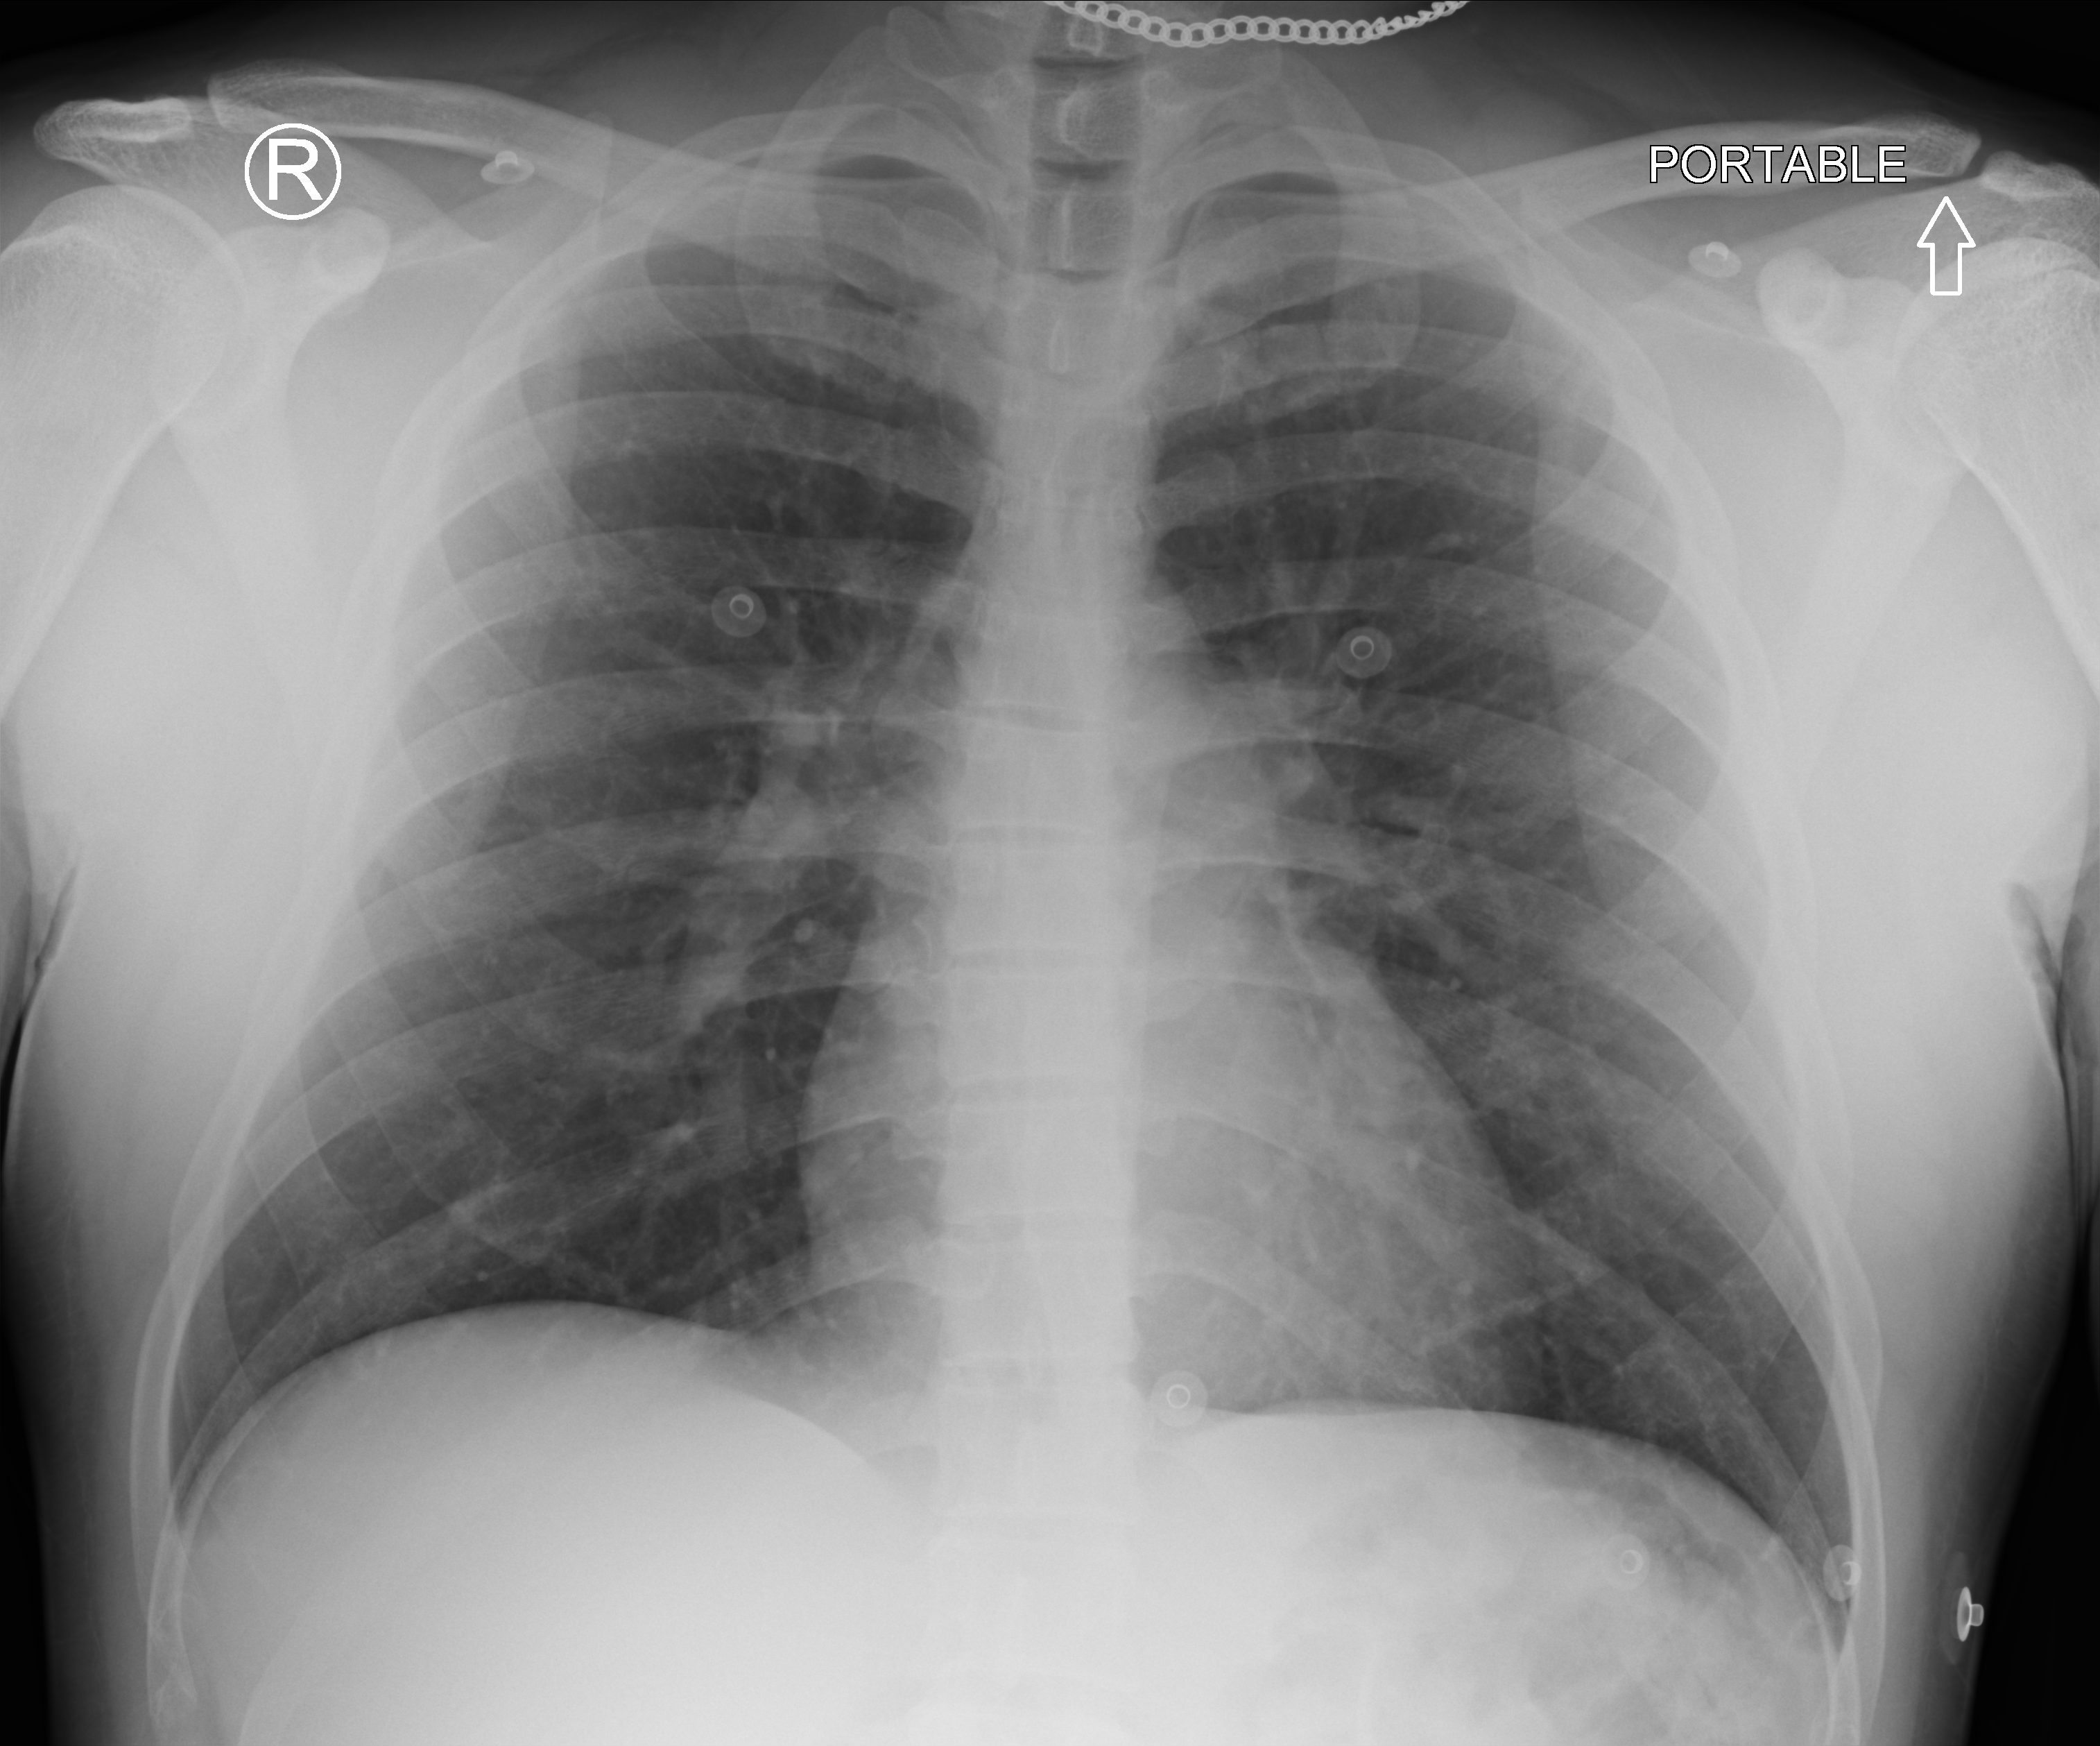
Chest X-ray (portable), anteroposterior (AP) projection. Male patient hospitalised with COVID-19, age 18–59 years.
Admission-level facts for this patient (not findings on this image; timing relative to this image not recorded):
- mechanically ventilated during this hospital stay: no